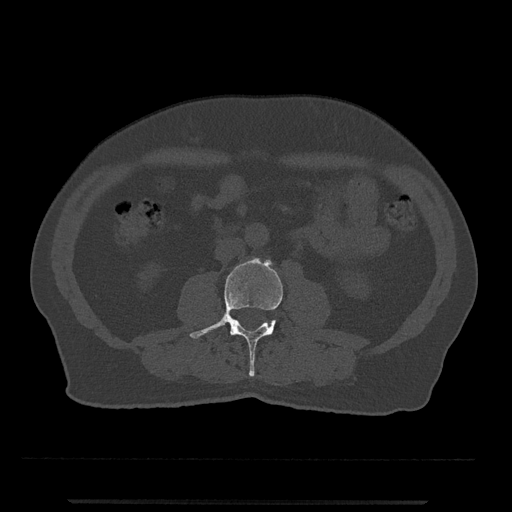
CT including the spine, one axial slice; position 197 of 797 along the scan axis; reconstruction kernel Br40s/3; 120 kVp; bone window (W 1800 / L 400 HU); 0.5 mm slice thickness; 512 × 512 image matrix, field of view 419 × 419 mm. Patient: male, 63 years. From the clinical record (not read from this slice): primary cancer: prostate.
Outlined on this slice (semi-automatically segmented with operator editing):
- L3 vertebra: bounding box (x1, y1, x2, y2) in pixels: (189, 258, 283, 377)